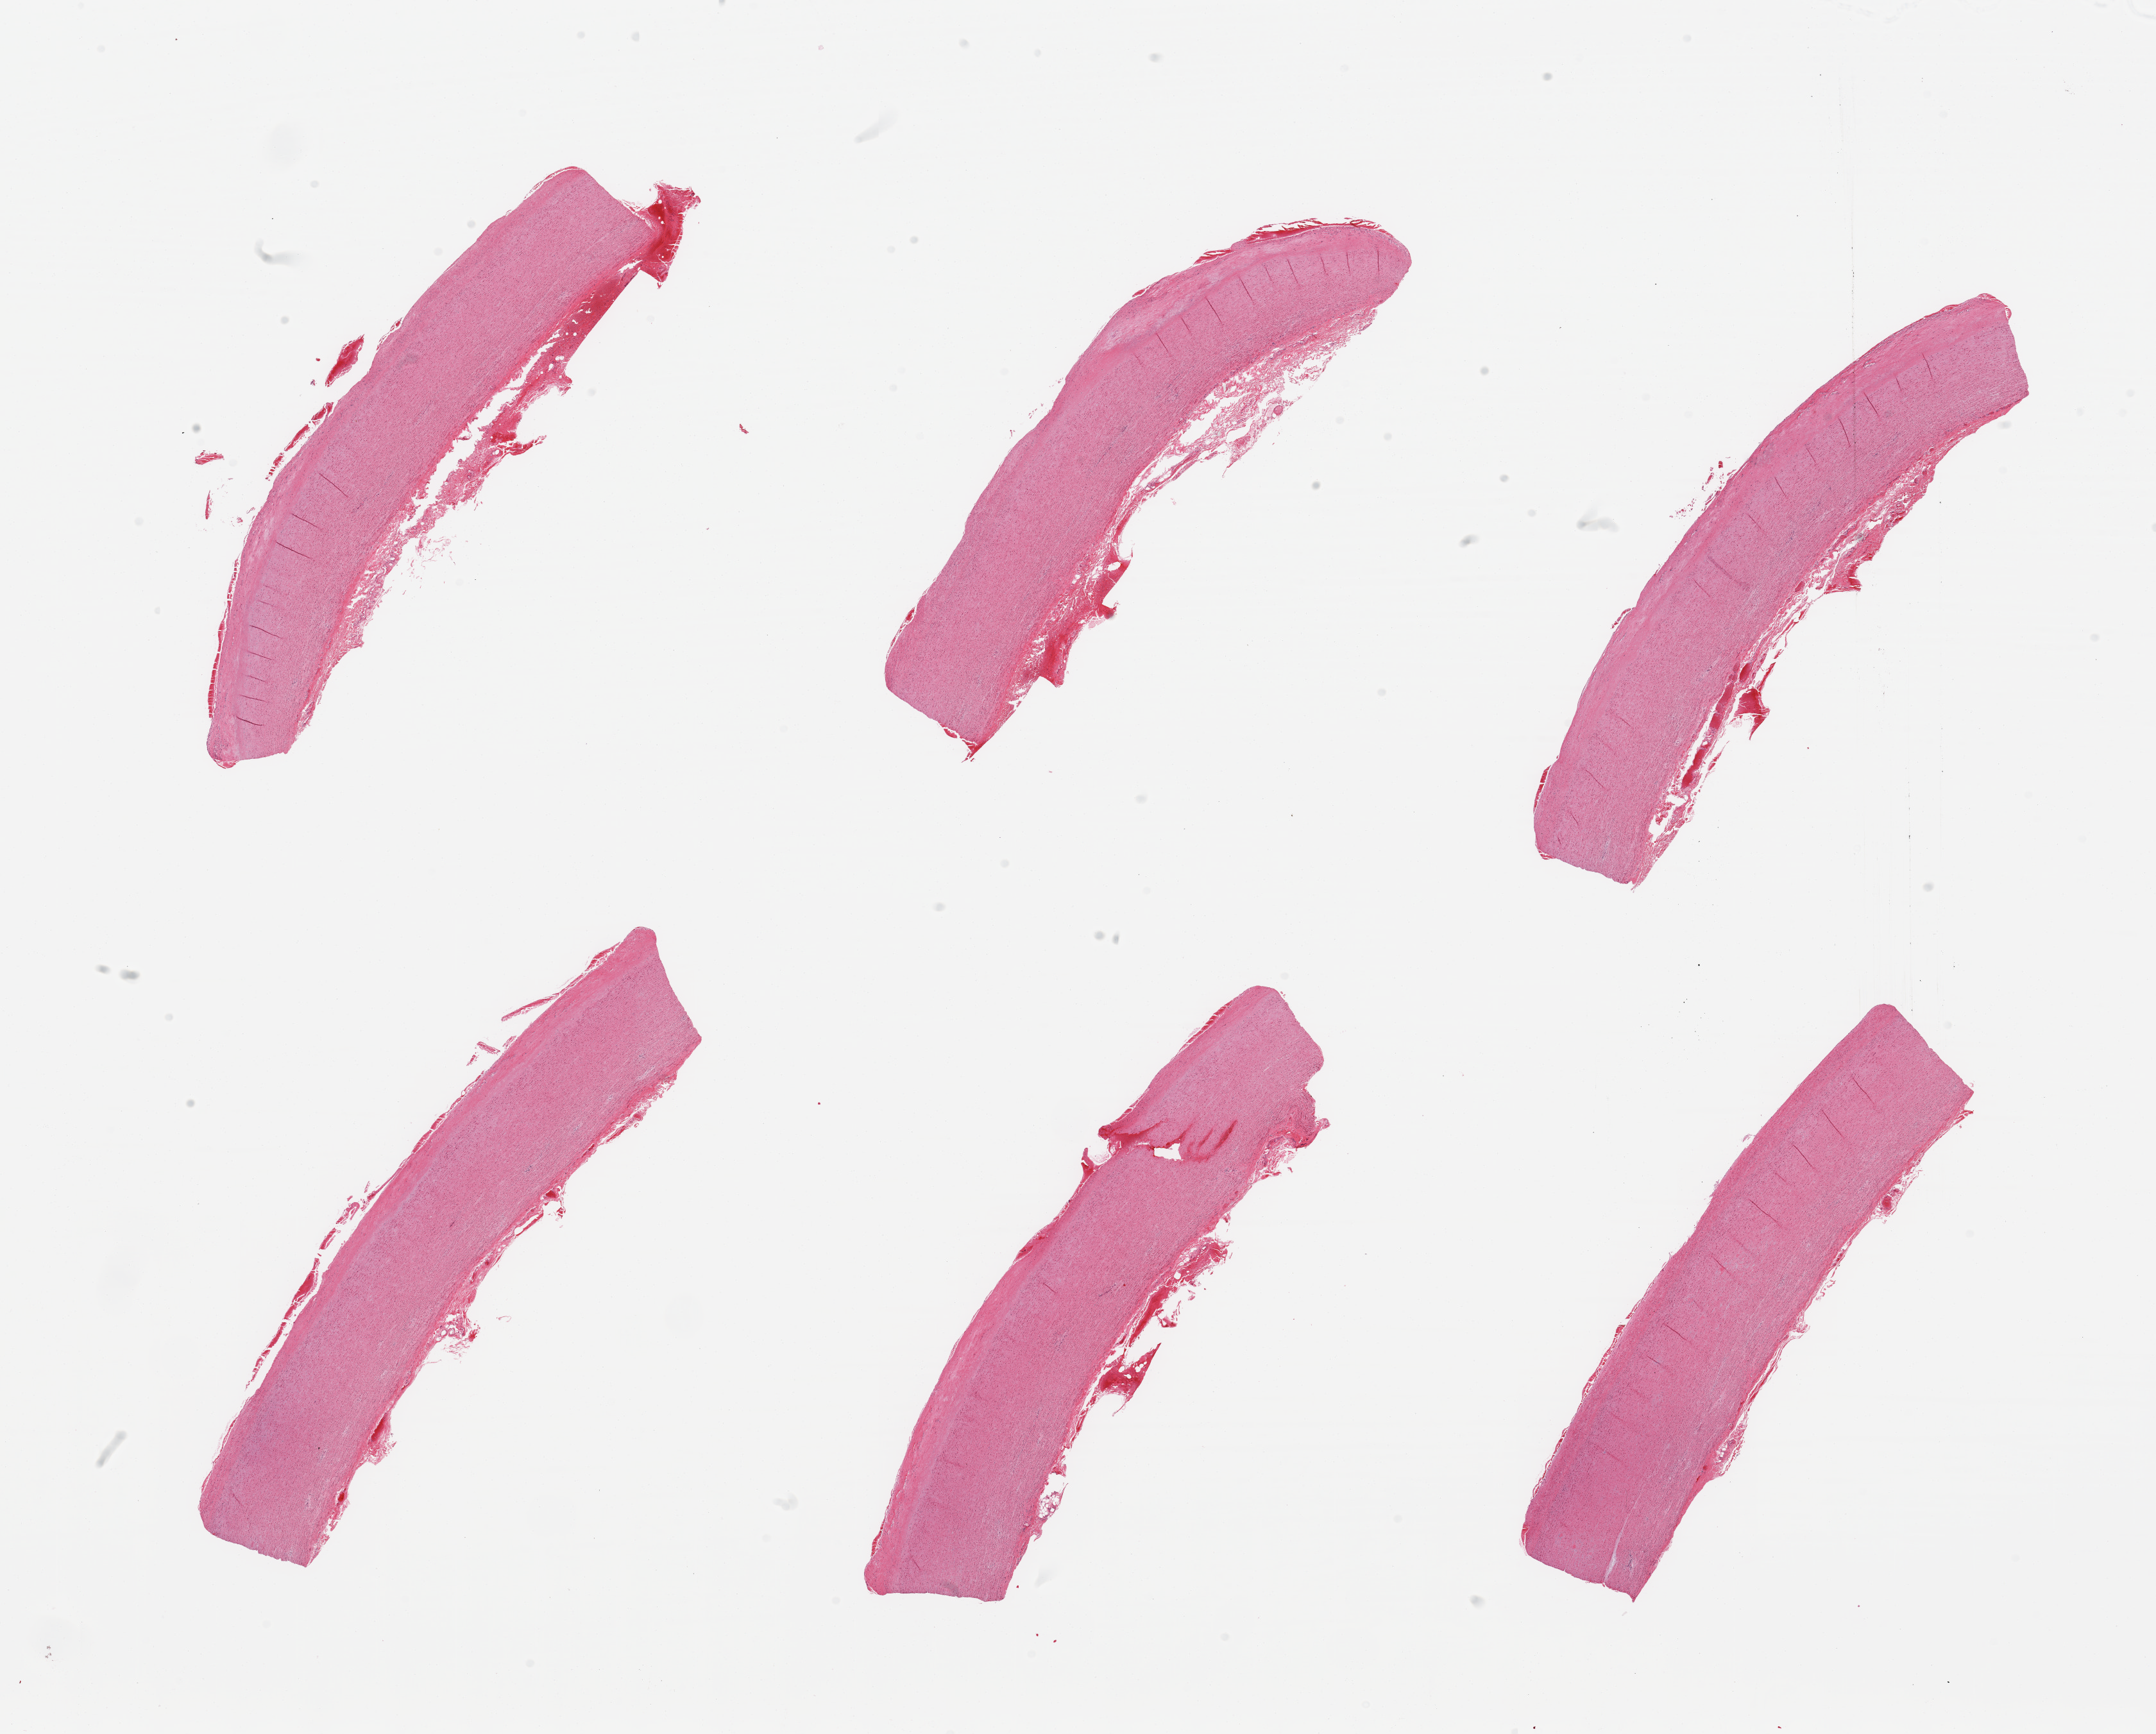
H&E whole-slide image — low-resolution overview of the scanned area, about 26.6 x 21.4 mm (acquisition: 20x scan), PAXgene-fixed, paraffin-embedded tissue, section of aorta (target tissue), donor tissue sample.
Pathologist's review note for this sample: 6 pieces; atherosclerosis.